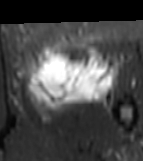
MRI of an extremity soft-tissue mass, one axial slice; slice 33 of 81 in the series (ordered by position); STIR; MR volume resampled by the dataset authors to the PET/CT grid (not the native acquisition matrix); 3.27 mm slice thickness; 143 × 161 image matrix, field of view 140 × 157 mm. Female patient. Case-level facts recorded for this patient, not image findings: histological type: myxofibrosarcoma; grade: intermediate; site of the primary tumour: left thigh.
Structures marked on this image (expert contour drawn on MRI and transferred to this co-registered scan by the dataset authors):
- gross tumour volume including surrounding oedema: bounding box <26,42,118,120> (left, top, right, bottom; pixels)
- gross tumour volume (mass): <28,42,114,102>